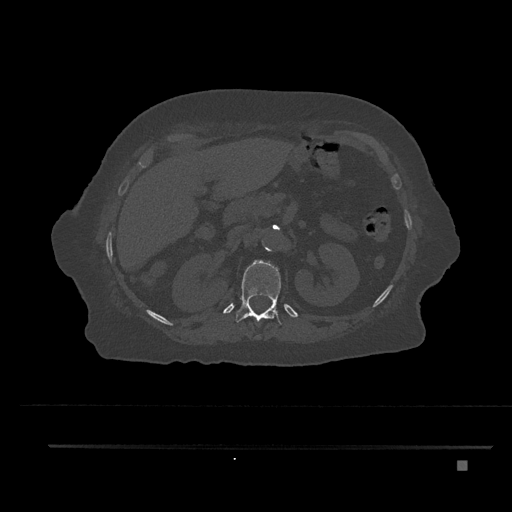
CT including the spine, one axial slice; position 263 of 797 along the scan axis; reconstruction kernel Br40s/3; 120 kVp; bone window (W 1800 / L 400 HU); 512 × 512 image matrix. Female patient, age 76 years. From the clinical record (not read from this slice): primary cancer: lung.
Outlined on this slice (semi-automatically segmented with operator editing):
- T12 vertebra: bounding box [x1, y1, x2, y2] px = [235, 261, 282, 337]